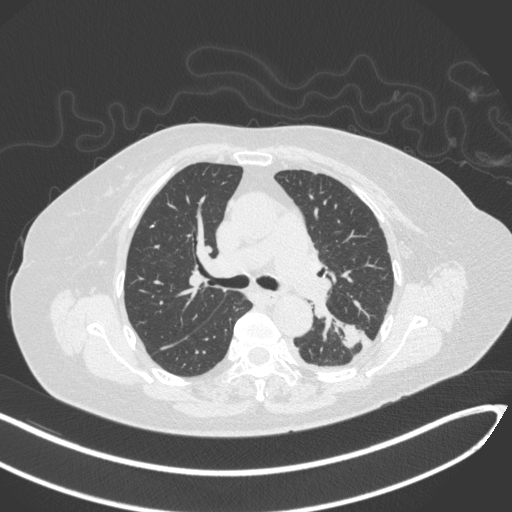
Chest CT, one axial slice; position 199 of 270 along the scan axis; 120 kVp; lung window (W 1500 / L -600 HU); 512 × 512 image matrix. Patient: female, 76 years. Case-level facts recorded for this patient, not image findings: clinical TNM (as recorded): T1c N0 M0.
Outlined on this slice (bounding box drawn by a radiologist):
- lung tumour (recorded histology: adenocarcinoma): box from (x=336, y=322) to (x=365, y=349) px